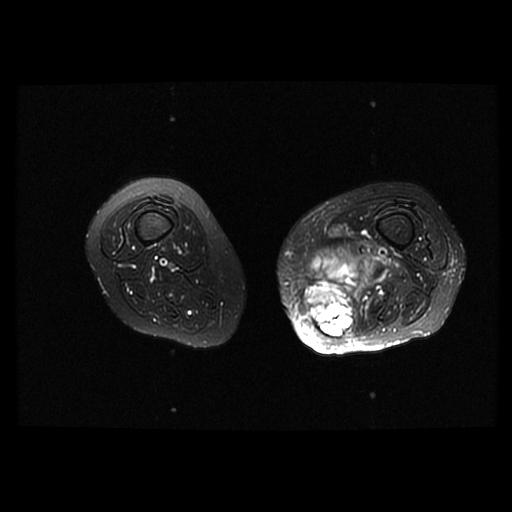
MRI of an extremity soft-tissue mass, one axial slice; position 24 of 42 along the scan axis; T2-weighted fat-saturated; 6 mm slice thickness; 512 × 512 image matrix, field of view 420 × 420 mm. Female patient. From the clinical record (not read from this slice): histological type: pleomorphic leiomyosarcoma; grade: high; site of the primary tumour: left thigh.
Outlined on this slice (outlined manually by an expert reader):
- gross tumour volume including surrounding oedema: bounding box [x1, y1, x2, y2] px = [303, 243, 383, 341]
- gross tumour volume (mass): [303, 280, 354, 337]